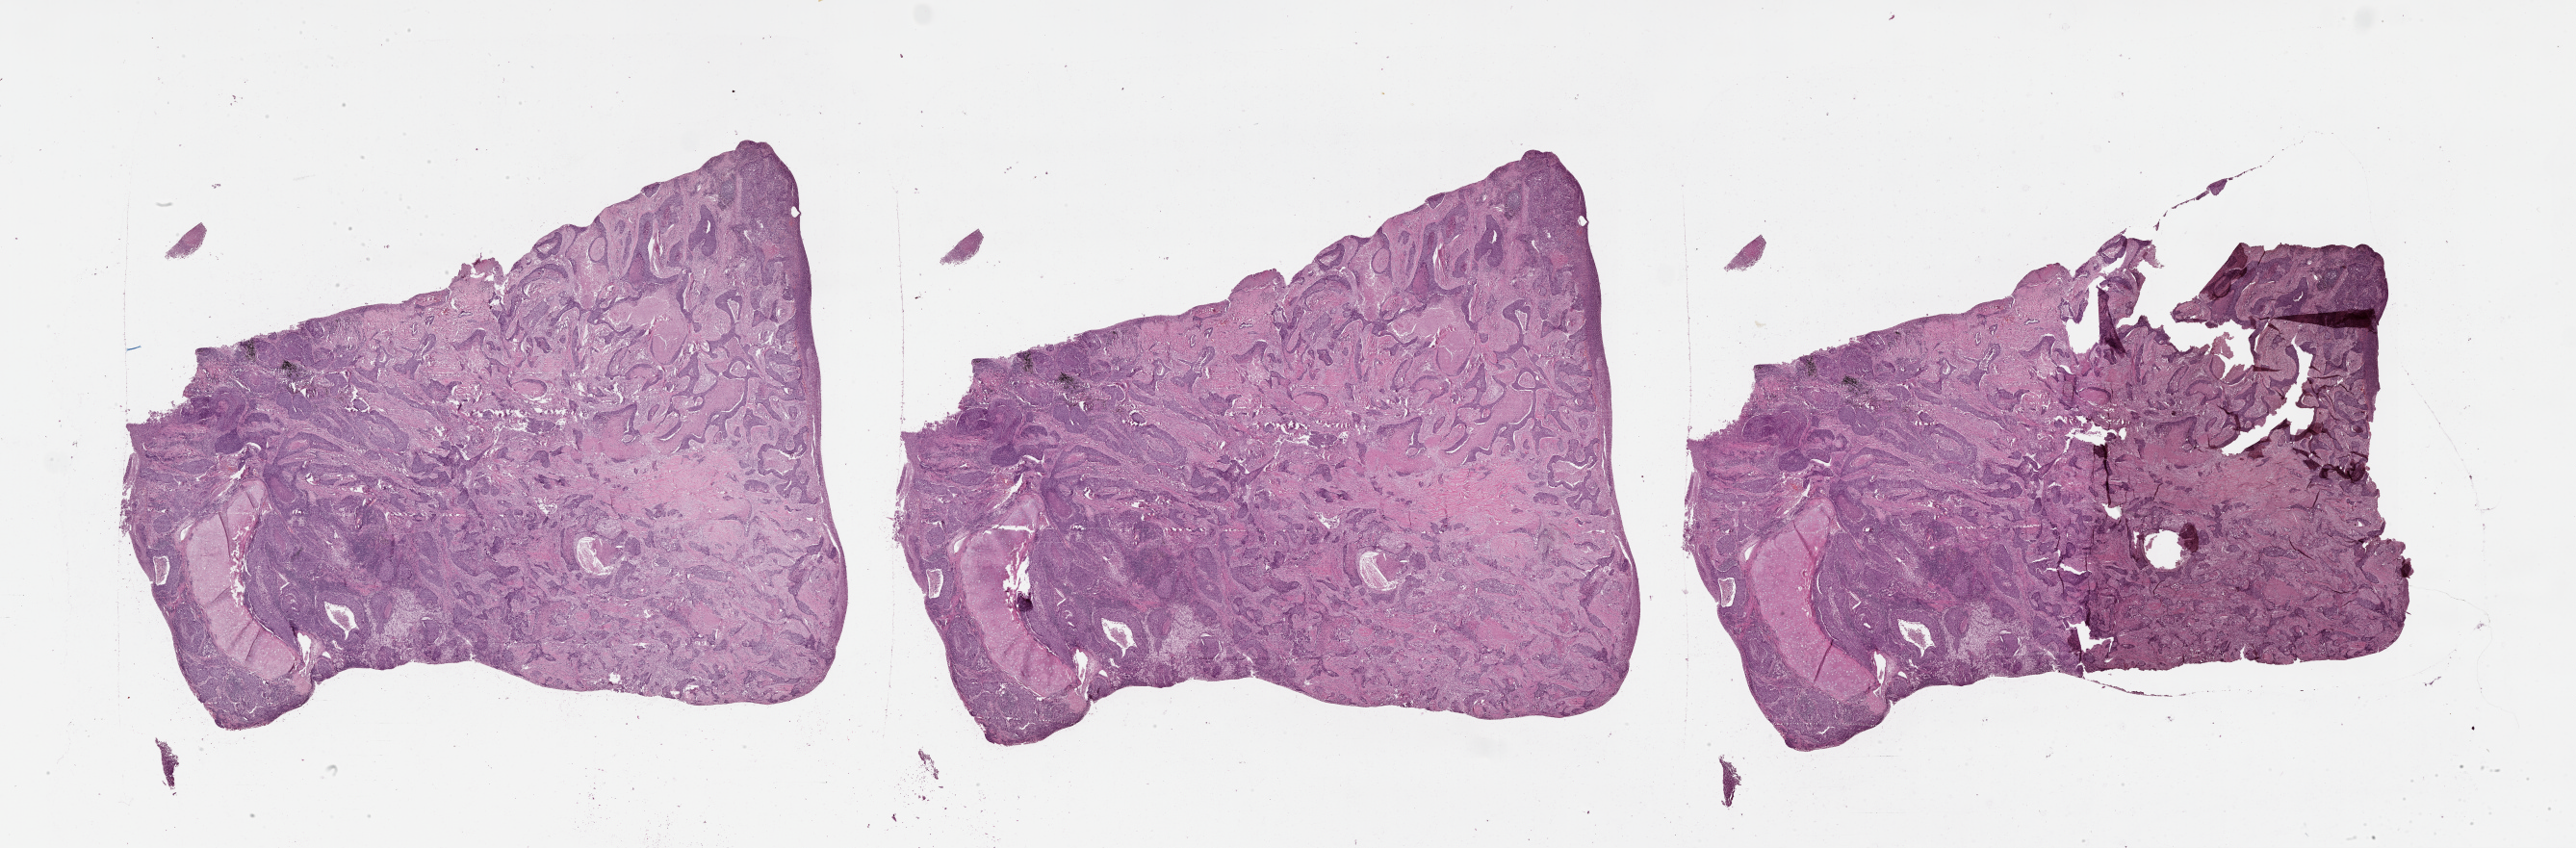
Whole-slide histology image, H&E-stained — low-resolution overview of the scanned area, about 43.1 x 14.2 mm; lung, tumour tissue. Patient: male, age 63 years.
Patient diagnosis (cohort enrolment): squamous cell carcinoma (lung).